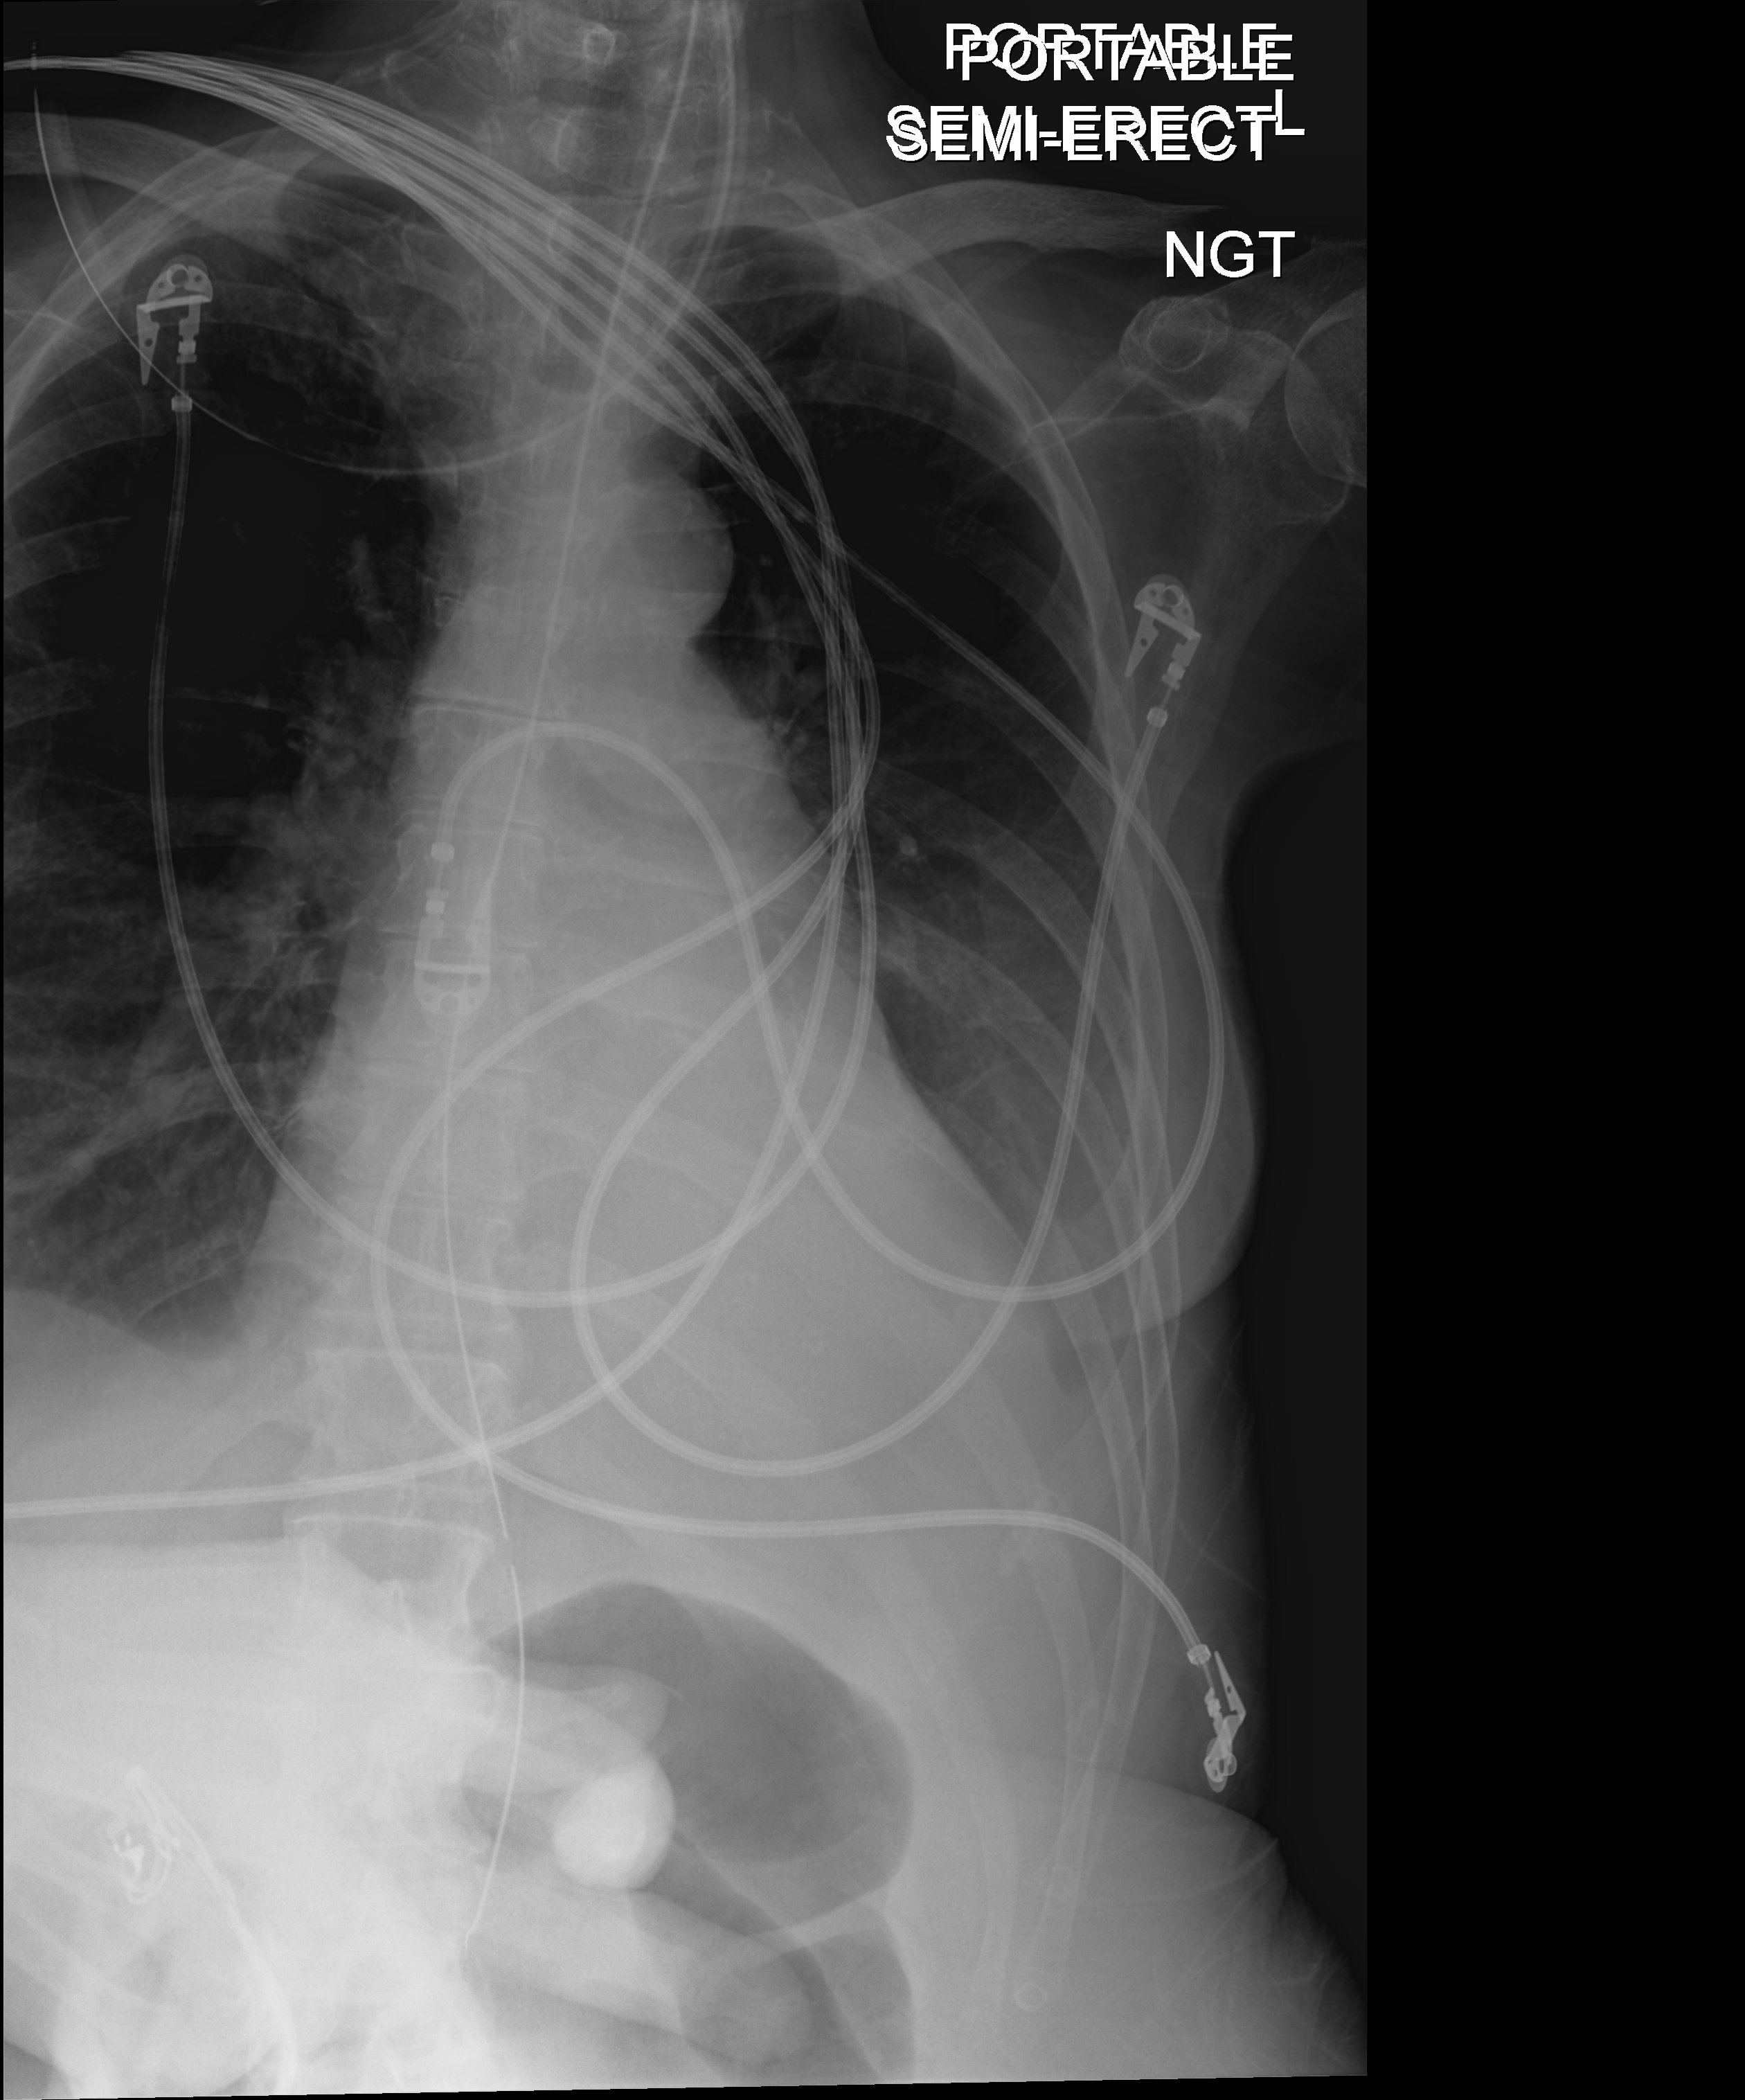
Portable chest radiograph, anteroposterior (AP) projection. Patient hospitalised with COVID-19; female, aged 60–74 years.
Admission-level facts for this patient (not findings on this image; timing relative to this image not recorded):
- admitted to intensive care during this hospital stay: yes
- mechanically ventilated during this hospital stay: yes